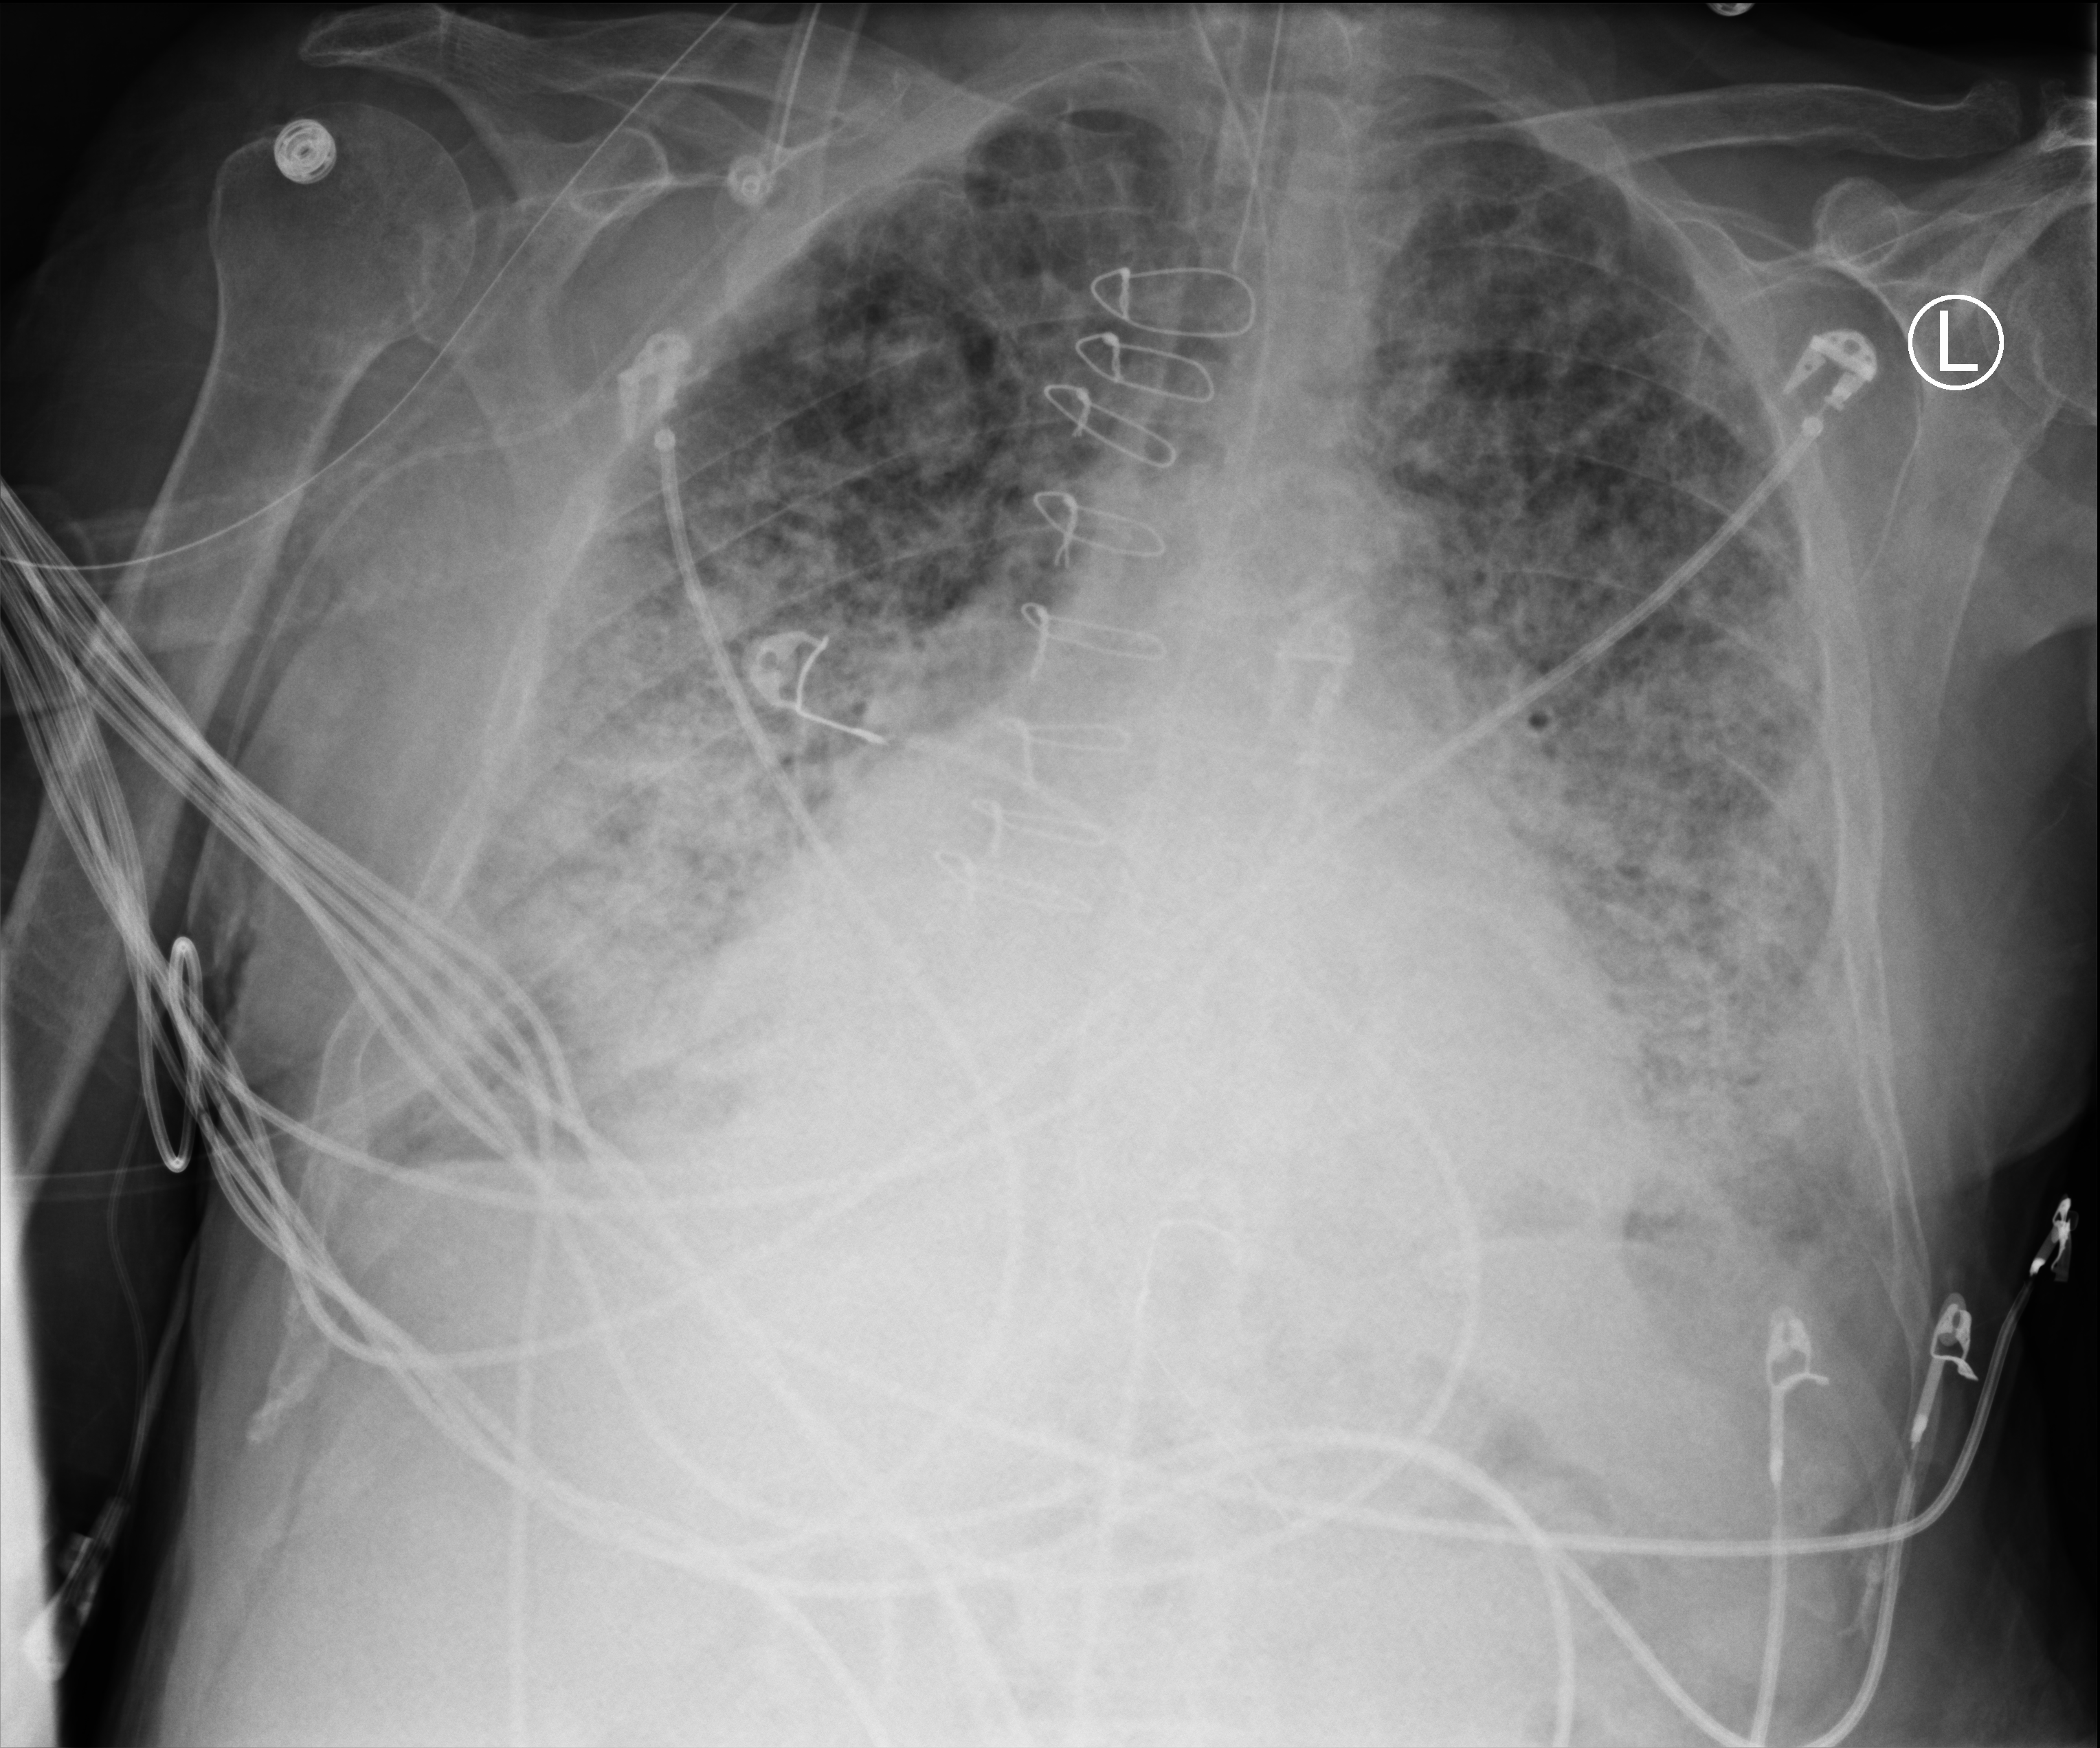
Chest X-ray (portable). Patient hospitalised with COVID-19; male, aged 75–90 years.
From the hospital-stay record, not from the radiograph (when in the stay this image was taken is not recorded):
- length of hospital stay: 40 days
- admitted to intensive care during this hospital stay: yes